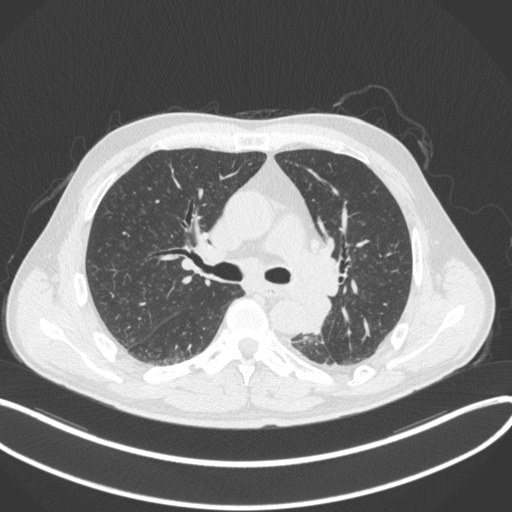
Chest CT, one axial slice. Slice 212 of 328 in the series (ordered by position). 120 kVp. Lung window (W 1500 / L -600 HU). 1 mm slice thickness. 512 × 512 image matrix, field of view 400 × 400 mm. Male patient, age 59 years. From the clinical record (not read from this slice): clinical TNM (as recorded): T2a N2 M0.
Outlined on this slice (bounding box drawn by a radiologist):
- lung tumour (recorded histology: squamous cell carcinoma): box from (x=305, y=286) to (x=331, y=336) px